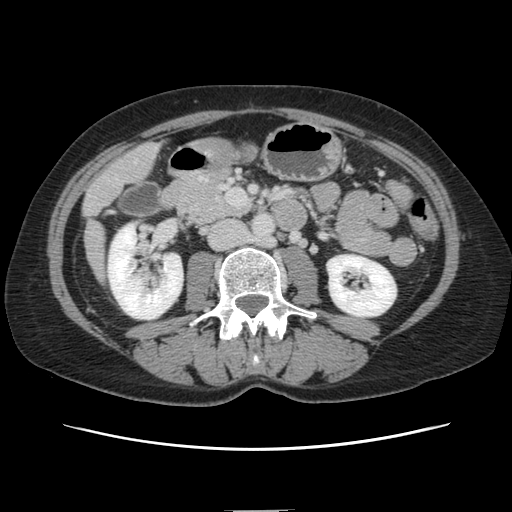
Contrast-enhanced abdominal CT, one axial slice; position 37 of 141 along the scan axis; 120 kVp; intravenous contrast given; soft-tissue window (W 400 / L 40 HU); 2.5 mm slice thickness; 512 × 512 image matrix. Female patient, age 63 years. Case-level facts recorded for this patient, not image findings: diagnosis: colorectal cancer liver metastases, imaged before liver resection; multiple liver metastases: yes; largest metastasis: 3.2 cm; chemotherapy before resection: yes.
Structures marked on this image (manually delineated by an expert):
- liver: bounding box <86,144,158,280> (left, top, right, bottom; pixels)